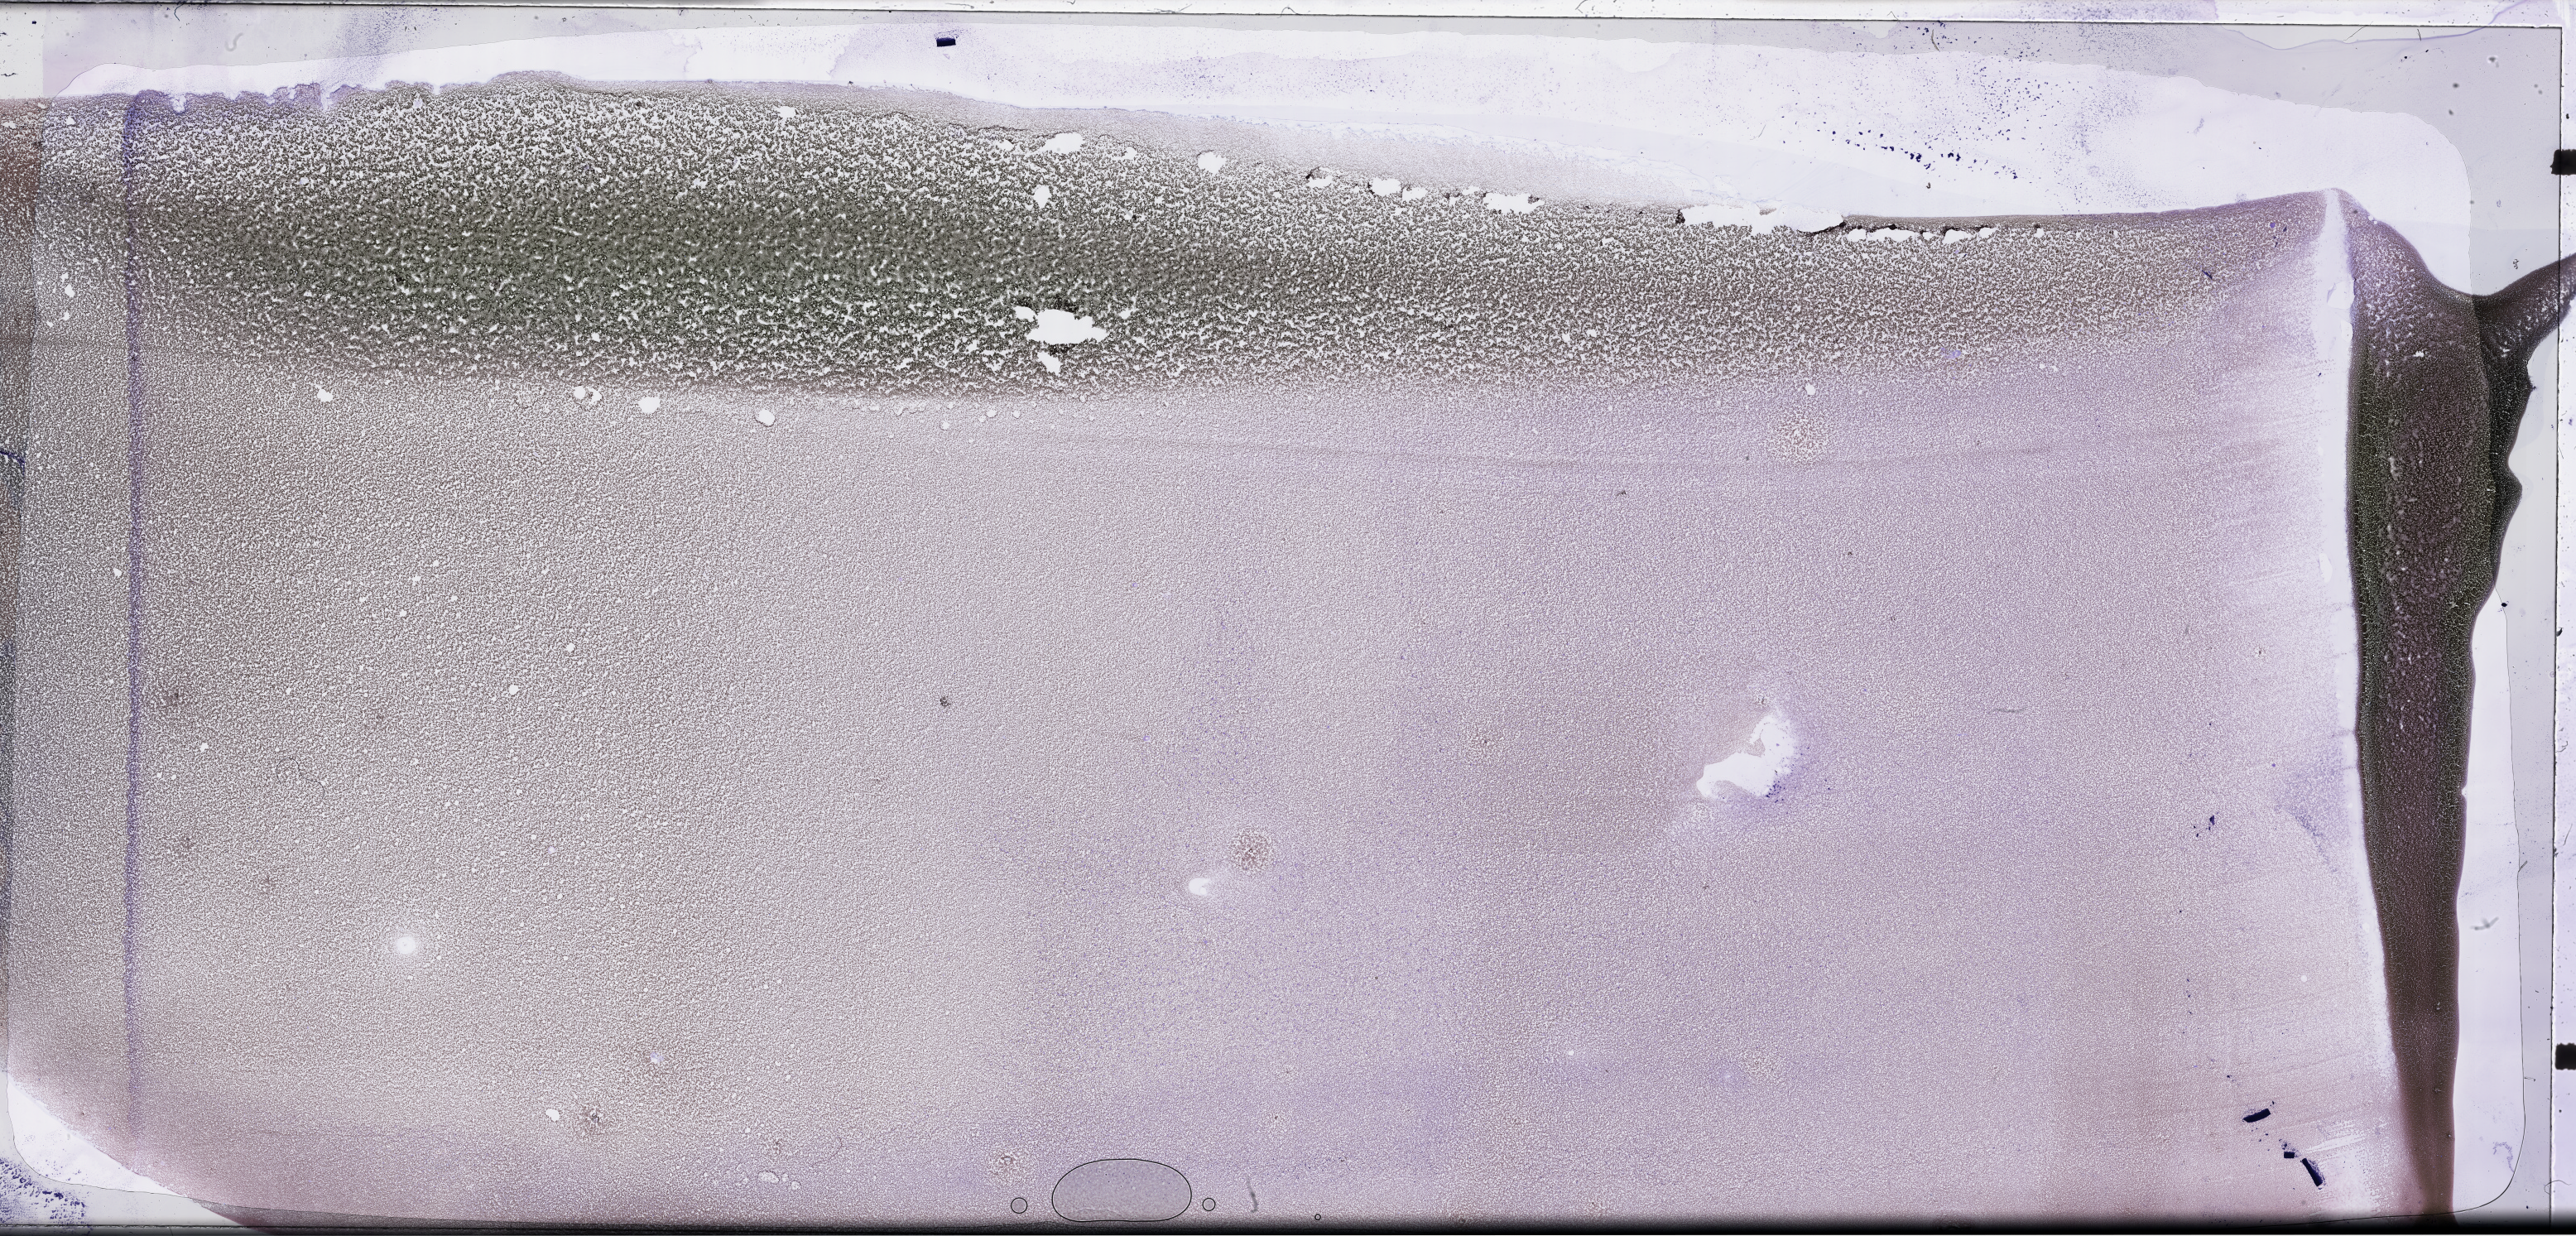
Whole-slide image of a bone marrow smear, Wright–Giemsa stain — whole scanned area (about 50.3 x 24.1 mm) shown as a low-resolution overview. Smear from an EDTA sample. Collected at disease progression. Female patient.
* from a patient with: Acute Myeloid Leukemia Not Otherwise Specified